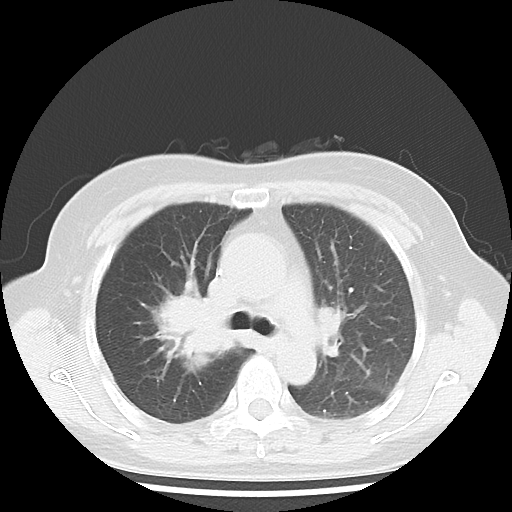
Chest CT, one axial slice. Position 27 of 43 along the scan axis. 100 kVp. Lung window (W 1500 / L -600 HU). 5 mm slice thickness. 512 × 512 image matrix, field of view 316 × 316 mm. Patient: female, 62 years. Case-level facts recorded for this patient, not image findings: clinical TNM (as recorded): T3 N0 M0; histopathological grade: G3.
Structures marked on this image (bounding box drawn by a radiologist):
- lung tumour (recorded histology: small cell carcinoma): bounding box [x1, y1, x2, y2] px = [130, 284, 242, 386]